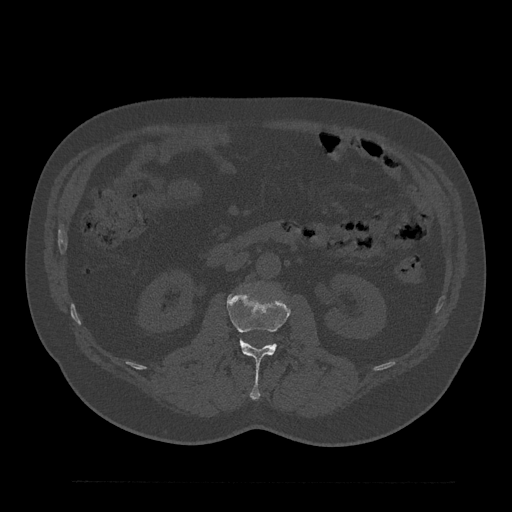
CT including the spine, one axial slice; position 91 of 797 along the scan axis; reconstruction kernel Br40s/3; 120 kVp; bone window (W 1800 / L 400 HU); 0.5 mm slice thickness; 512 × 512 image matrix, field of view 430 × 430 mm. Patient: male, 61 years. From the clinical record (not read from this slice): primary cancer: prostate.
Structures marked on this image (semi-automatic segmentation, software-assisted and operator-edited):
- L2 vertebra: bounding box (x1, y1, x2, y2) in pixels: (227, 288, 290, 399)